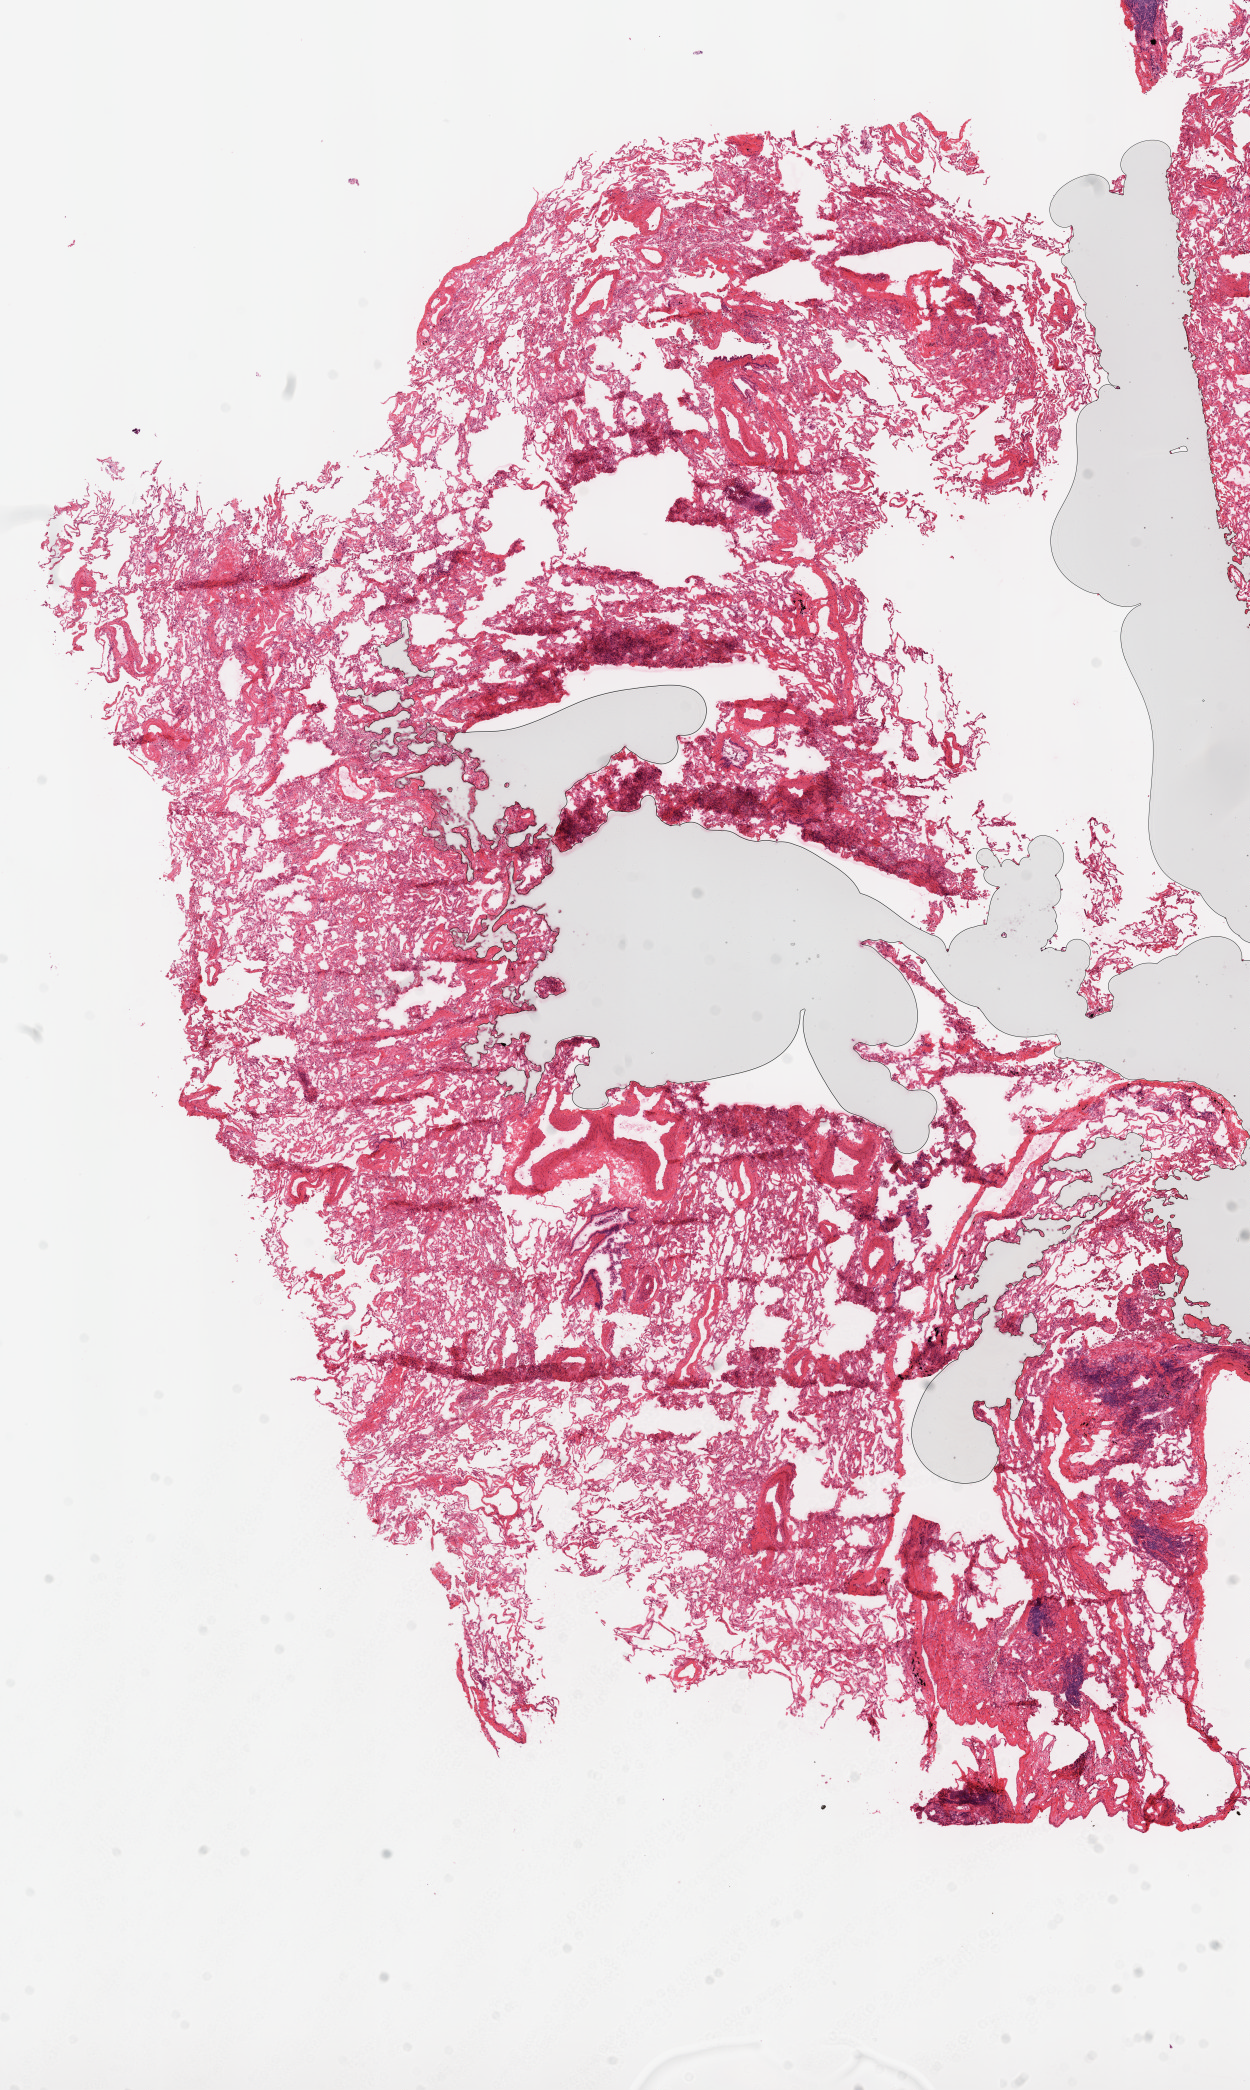
H&E-stained whole-slide image, a low-resolution overview of the entire scanned area, about 10.0 x 16.8 mm (from a 20x scan), frozen section, lung, solid tissue normal (non-tumour tissue) sample. Male, age 76 years at initial diagnosis.
This section: solid tissue normal sample (biorepository sample class). Patient diagnosis: Squamous cell carcinoma, NOS (upper lobe, lung).